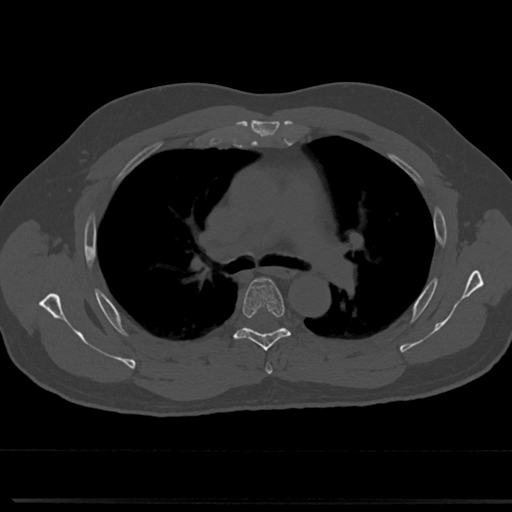
CT including the spine, one axial slice; slice 499 of 817 in the series (ordered by position); reconstruction kernel Br40s/3; 120 kVp; bone window (W 1800 / L 400 HU); 0.5 mm slice thickness; 512 × 512 image matrix. Male patient, age 61 years. Case-level facts recorded for this patient, not image findings: primary cancer: prostate.
Outlined on this slice (semi-automatic segmentation, software-assisted and operator-edited):
- T4 vertebra: bounding box <264,355,273,374> (left, top, right, bottom; pixels)
- T5 vertebra: <218,277,308,351>